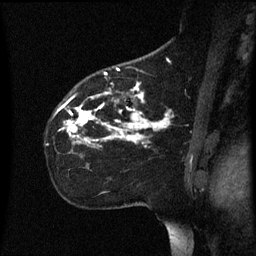
Breast MRI (dynamic contrast-enhanced), one sagittal slice; slice 41 of 60 in the series (ordered by position); dynamic contrast-enhanced series, image 2 of 3 at this slice position (ordered by acquisition); 1.5 T; TE 4.2 ms, TR 8.4 ms; 2.2 mm slice thickness; 256 × 256 image matrix, field of view 200 × 200 mm. Patient: female, 35 years. Case-level facts recorded for this patient, not image findings: setting: breast cancer imaged before/during neoadjuvant chemotherapy; receptor status: HER2-positive.
Structures marked on this image (semi-automatic segmentation, software-assisted and operator-edited):
- analysis volume of interest (the breast-tissue region the enhancement analysis was run in; not a lesion): bounding box (x1, y1, x2, y2) in pixels: (47, 78, 172, 157)
- tumour enhancement mask (voxels above the 70 % enhancement threshold inside the analysis volume of interest): (62, 84, 171, 143)